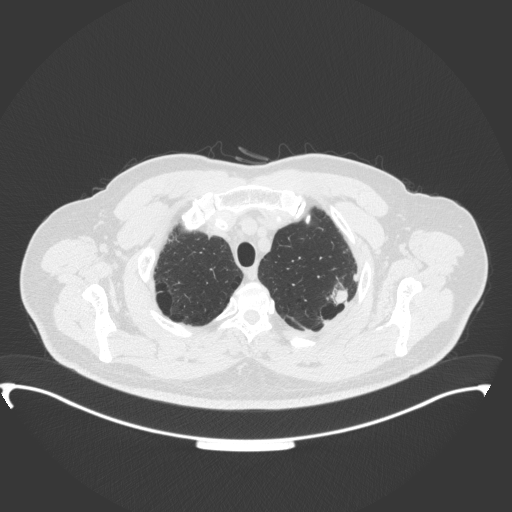
Chest CT, one axial slice. Slice 315 of 350 in the series (ordered by position). Reconstruction kernel B31f. 120 kVp. Lung window (W 1500 / L -600 HU). 1 mm slice thickness. 512 × 512 image matrix, field of view 459 × 459 mm. Patient: male, 64 years. From the clinical record (not read from this slice): clinical TNM (as recorded): T1c N1 M1.
Outlined on this slice (rectangle marked by the reading radiologist):
- lung tumour (recorded histology: adenocarcinoma): bounding box <327,278,350,311> (left, top, right, bottom; pixels)